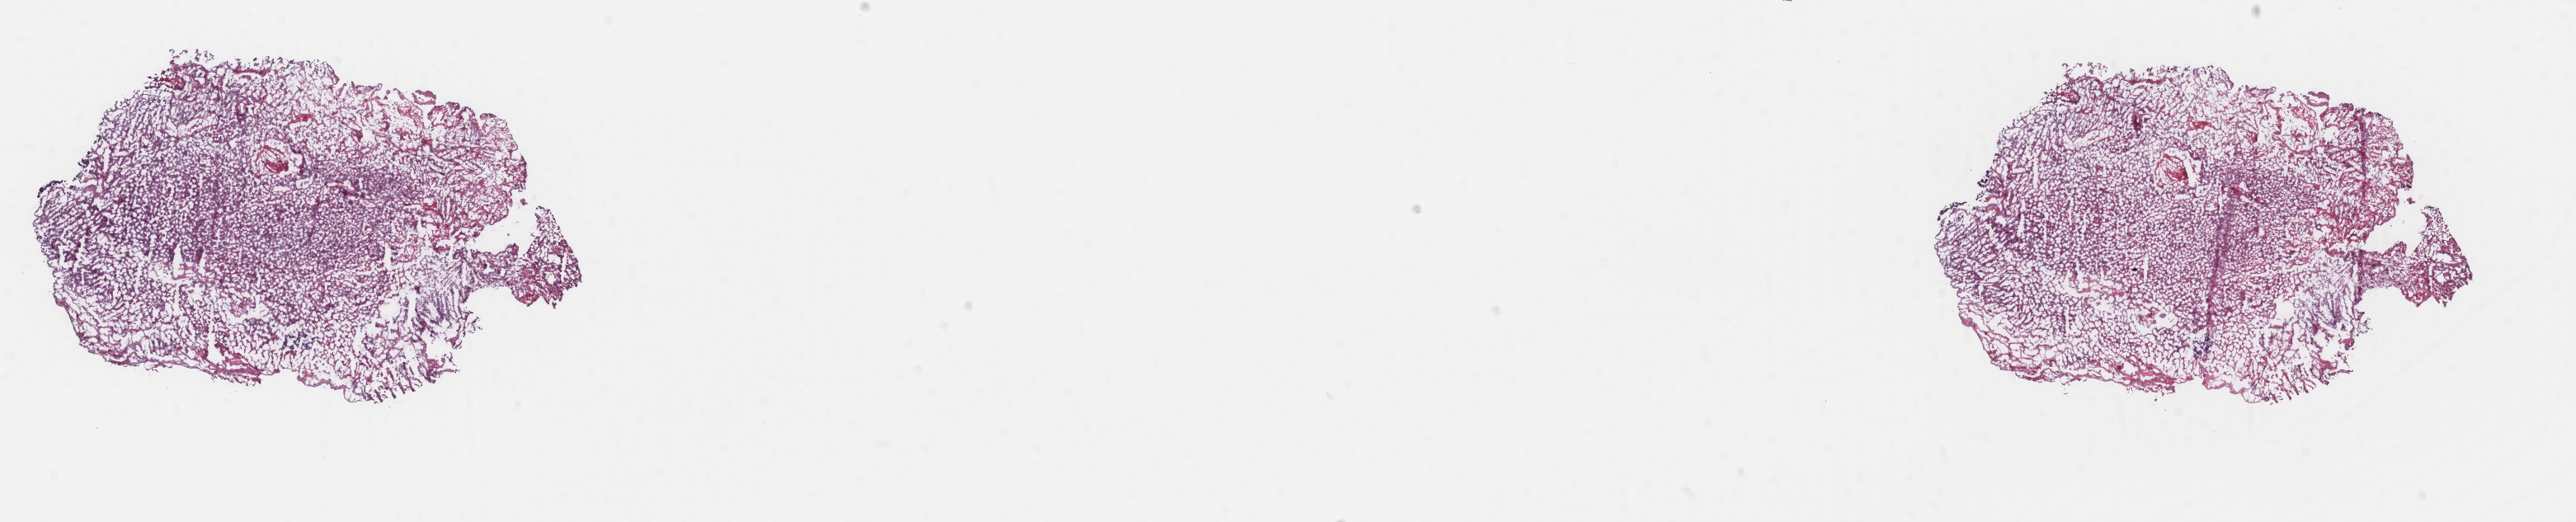
Digitized H&E-stained tissue section (whole slide), low-resolution overview of the scanned area, about 24.8 x 5.0 mm (acquisition: 40x scan). Frozen section from the top of the tissue portion. Uterus, primary tumour sample. Female patient; age at initial diagnosis 74 years. Slide review estimates, as recorded: tumour cells 95%, tumour nuclei 95%, normal cells 0%, stromal cells 0%, necrosis 5%. Infiltration values recorded for this section: lymphocyte infiltration 40%, monocyte infiltration 20%, neutrophil infiltration 20%.
Lymph nodes positive (case pathology): 0 of 22 examined. FIGO stage: IC. Pathologic diagnosis: Mullerian mixed tumor (endometrium).